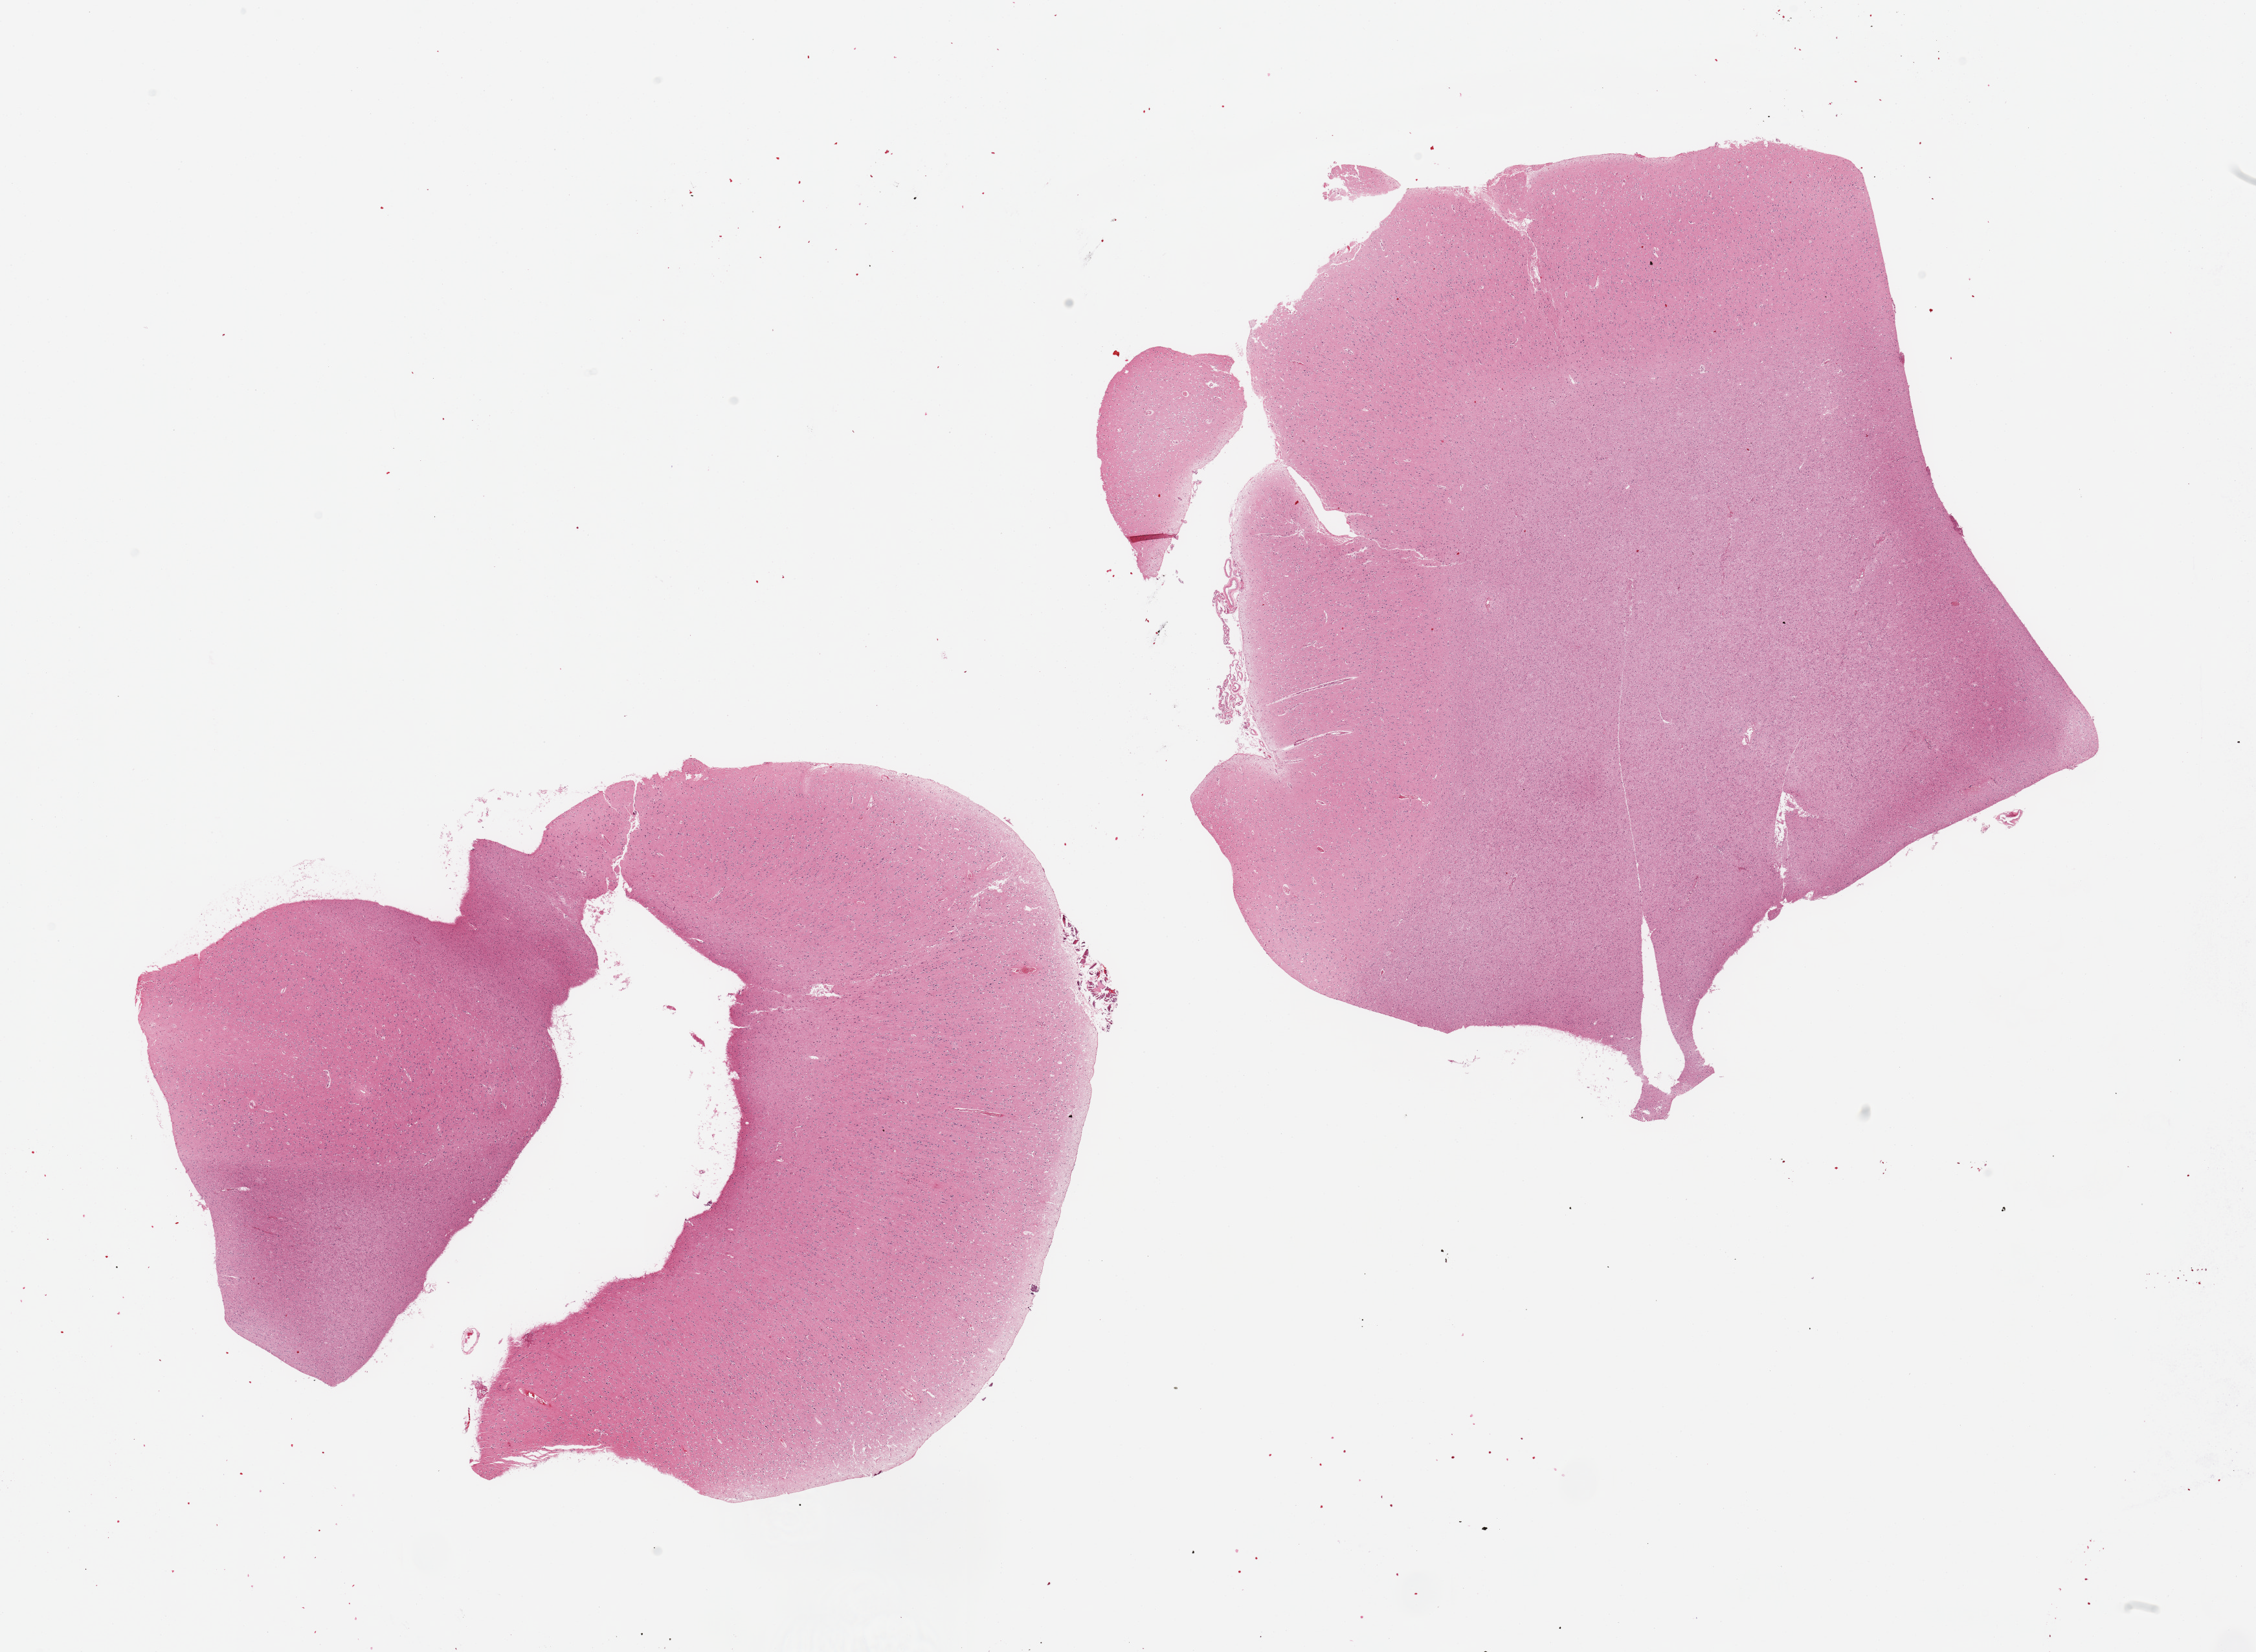
Hematoxylin and eosin (H&E) whole-slide image, a low-resolution overview of the entire scanned area, about 27.6 x 20.2 mm. PAXgene-fixed, paraffin-embedded tissue. Sampled site (target tissue): cerebral cortex. Tissue donor sample. Donor: male.
Review note (as recorded): 2 pieces, no abnormalities.